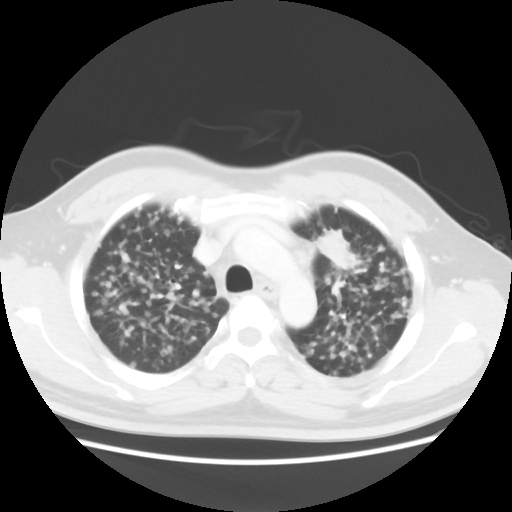
Chest CT, one axial slice. Reconstruction kernel STANDARD. Lung window (W 1500 / L -600 HU). 5 mm slice thickness. 512 × 512 image matrix. Male patient, age 41 years. Case-level facts recorded for this patient, not image findings: clinical TNM (as recorded): T1c N3 M1b; histopathological grade: G2-3.
Outlined on this slice (rectangle marked by the reading radiologist):
- lung tumour (recorded histology: adenocarcinoma): bounding box <316,228,359,285> (left, top, right, bottom; pixels)